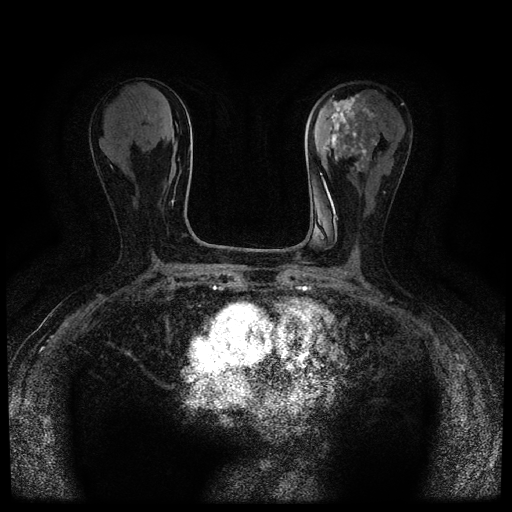
Breast MRI (dynamic contrast-enhanced, multi-phase), one axial slice; slice 40 of 116 in the series (ordered by position); dynamic contrast-enhanced series, time point 2 of 5 at this slice position (early post-contrast); 1.5 T; TE 2.7 ms, TR 5.4 ms; 2 mm slice thickness; 512 × 512 image matrix. Female patient, age 80 years.
Outlined on this slice (semi-automatically segmented with operator editing):
- breast lesion (labelled 'tumour' in the annotation; benign lesions carry a separate 'benign' label): bounding box [x1, y1, x2, y2] px = [323, 94, 379, 173]